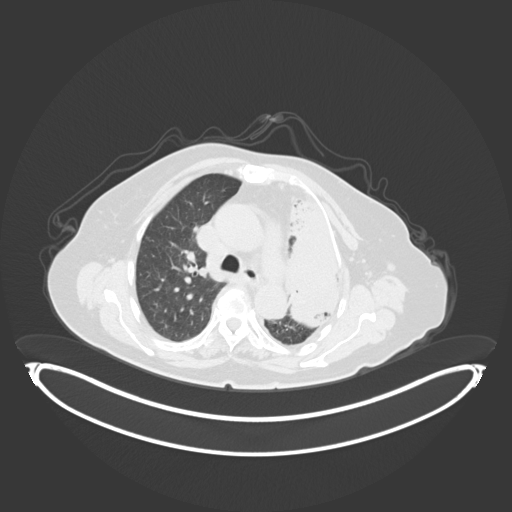
Chest CT, one axial slice; position 213 of 284 along the scan axis; reconstruction kernel B30f; 120 kVp; lung window (W 1500 / L -600 HU); 512 × 512 image matrix, field of view 500 × 500 mm. Patient: female, 75 years. From the clinical record (not read from this slice): clinical TNM (as recorded): T3 N3 M1.
Outlined on this slice (rectangle marked by the reading radiologist):
- lung tumour (recorded histology: adenocarcinoma): bounding box [x1, y1, x2, y2] px = [282, 196, 352, 337]